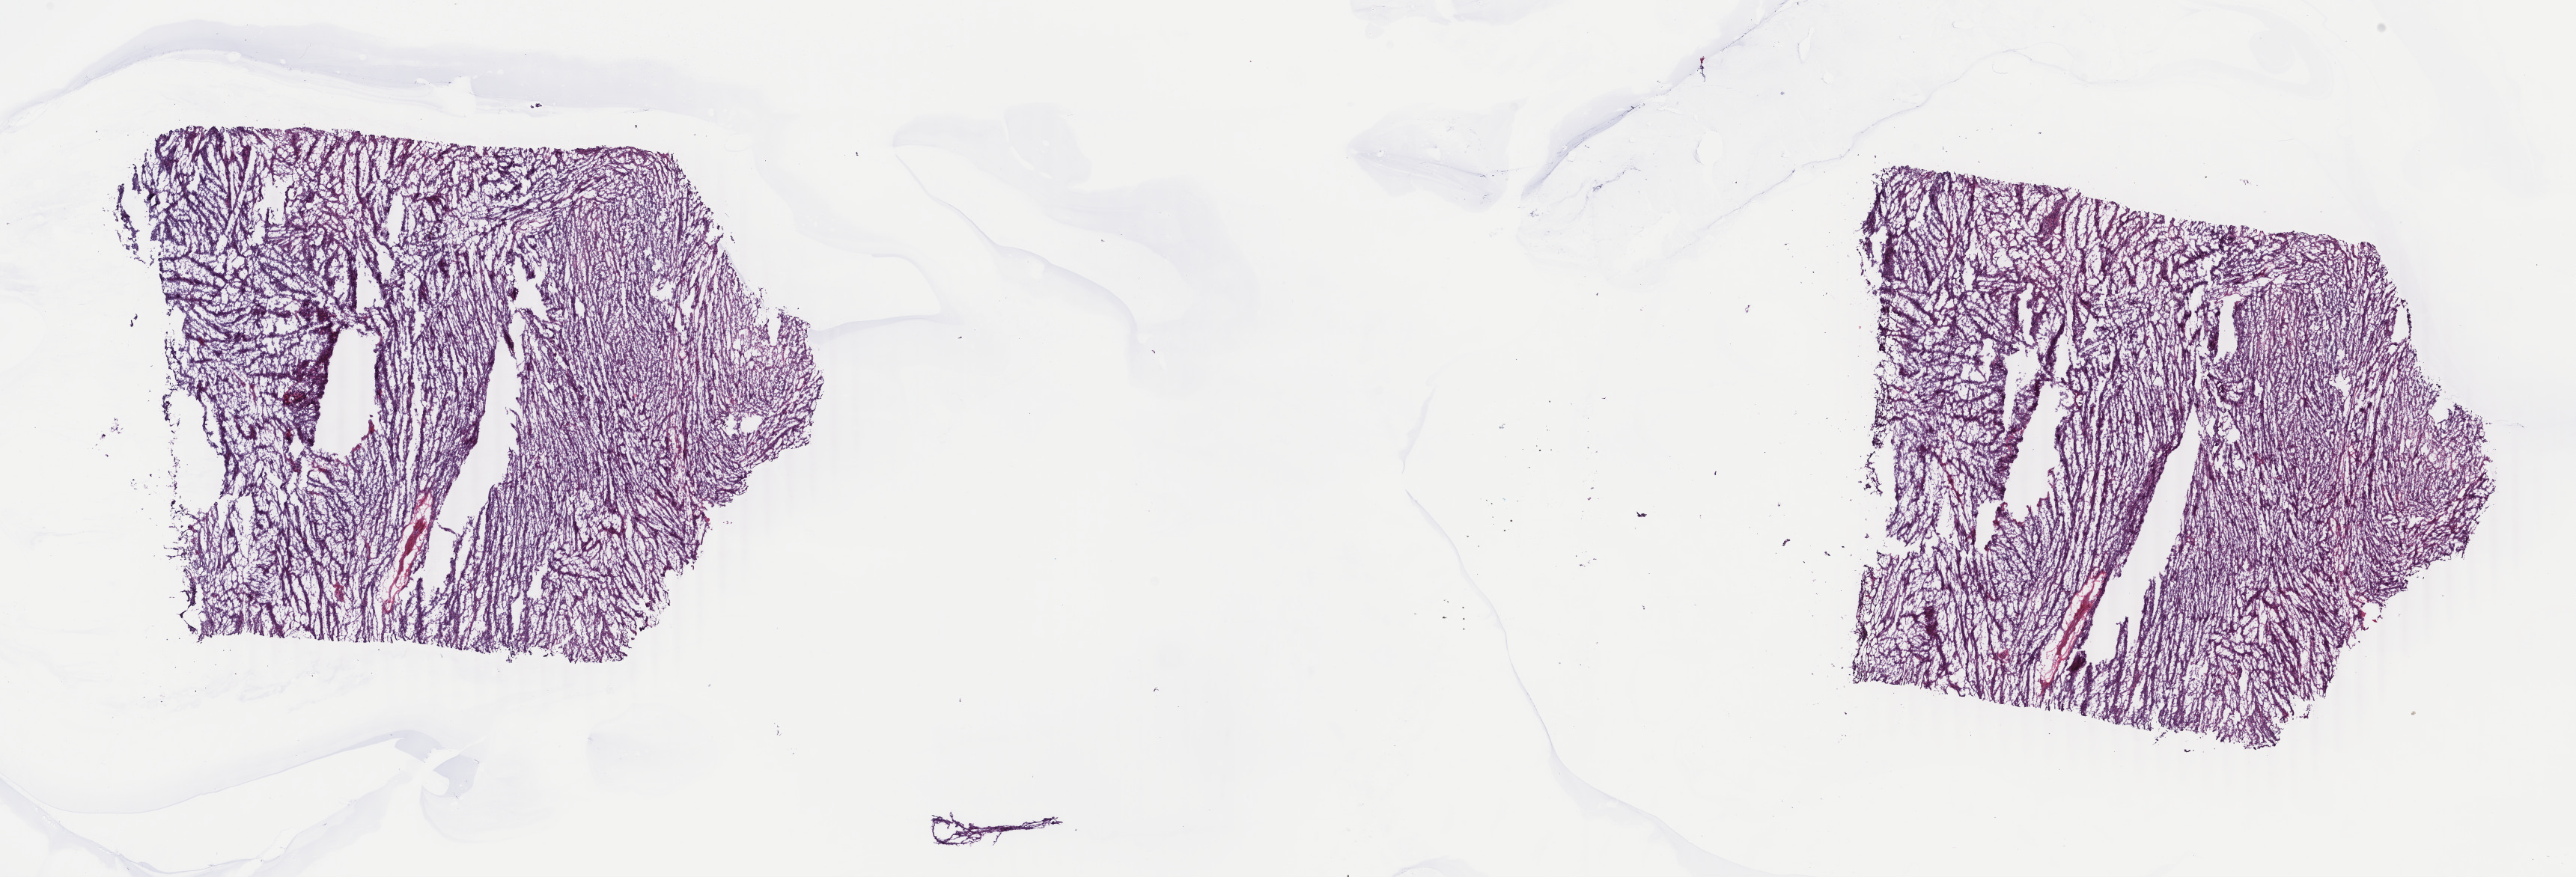
Digitized H&E tissue section (whole slide), low-resolution overview of the scanned area, about 27.4 x 9.3 mm, frozen section, sample: primary tumour, connective, subcutaneous and other soft tissues. Patient: female, age at initial diagnosis 28 years. Composition of this section per pathologist review: tumour cells 100%, tumour nuclei 95%.
Diagnosis: Synovial sarcoma, spindle cell (connective, subcutaneous and other soft tissues of lower limb and hip).